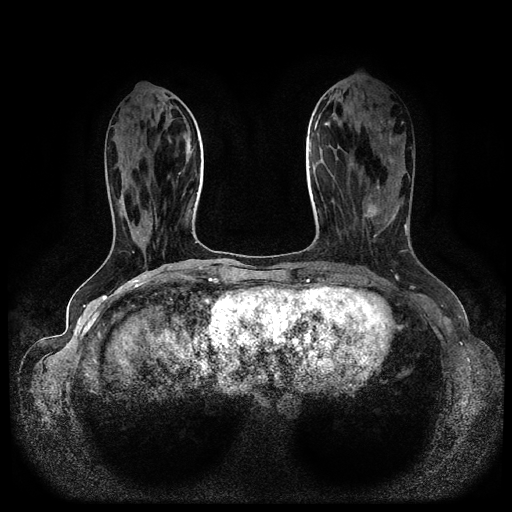
Breast MRI (dynamic contrast-enhanced, multi-phase), one axial slice; slice 35 of 116 in the series (ordered by position); dynamic contrast-enhanced series, time point 2 of 5 at this slice position (early post-contrast); 1.5 T; TE 2.6 ms, TR 5.3 ms; 2 mm slice thickness; 512 × 512 image matrix, field of view 350 × 350 mm. Female patient, age 45 years.
Annotated regions visible in this slice (semi-automatically segmented with operator editing):
- breast lesion (labelled 'tumour' in the annotation; benign lesions carry a separate 'benign' label): bounding box <362,199,380,224> (left, top, right, bottom; pixels)